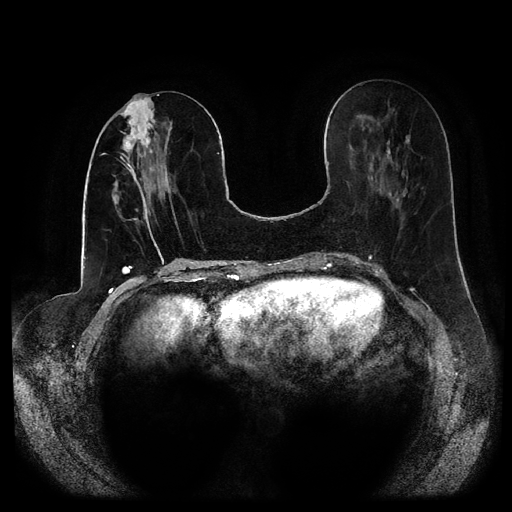
Breast MRI (dynamic contrast-enhanced, multi-phase), one axial slice; dynamic contrast-enhanced series, time point 2 of 5 at this slice position (early post-contrast); 1.5 T; TE 2.6 ms, TR 5.2 ms; 2 mm slice thickness; 512 × 512 image matrix, field of view 380 × 380 mm. Patient: female, 53 years.
Annotated regions visible in this slice (semi-automatic segmentation, software-assisted and operator-edited):
- breast lesion (labelled 'tumour' in the annotation; benign lesions carry a separate 'benign' label): box from (x=120, y=96) to (x=157, y=157) px